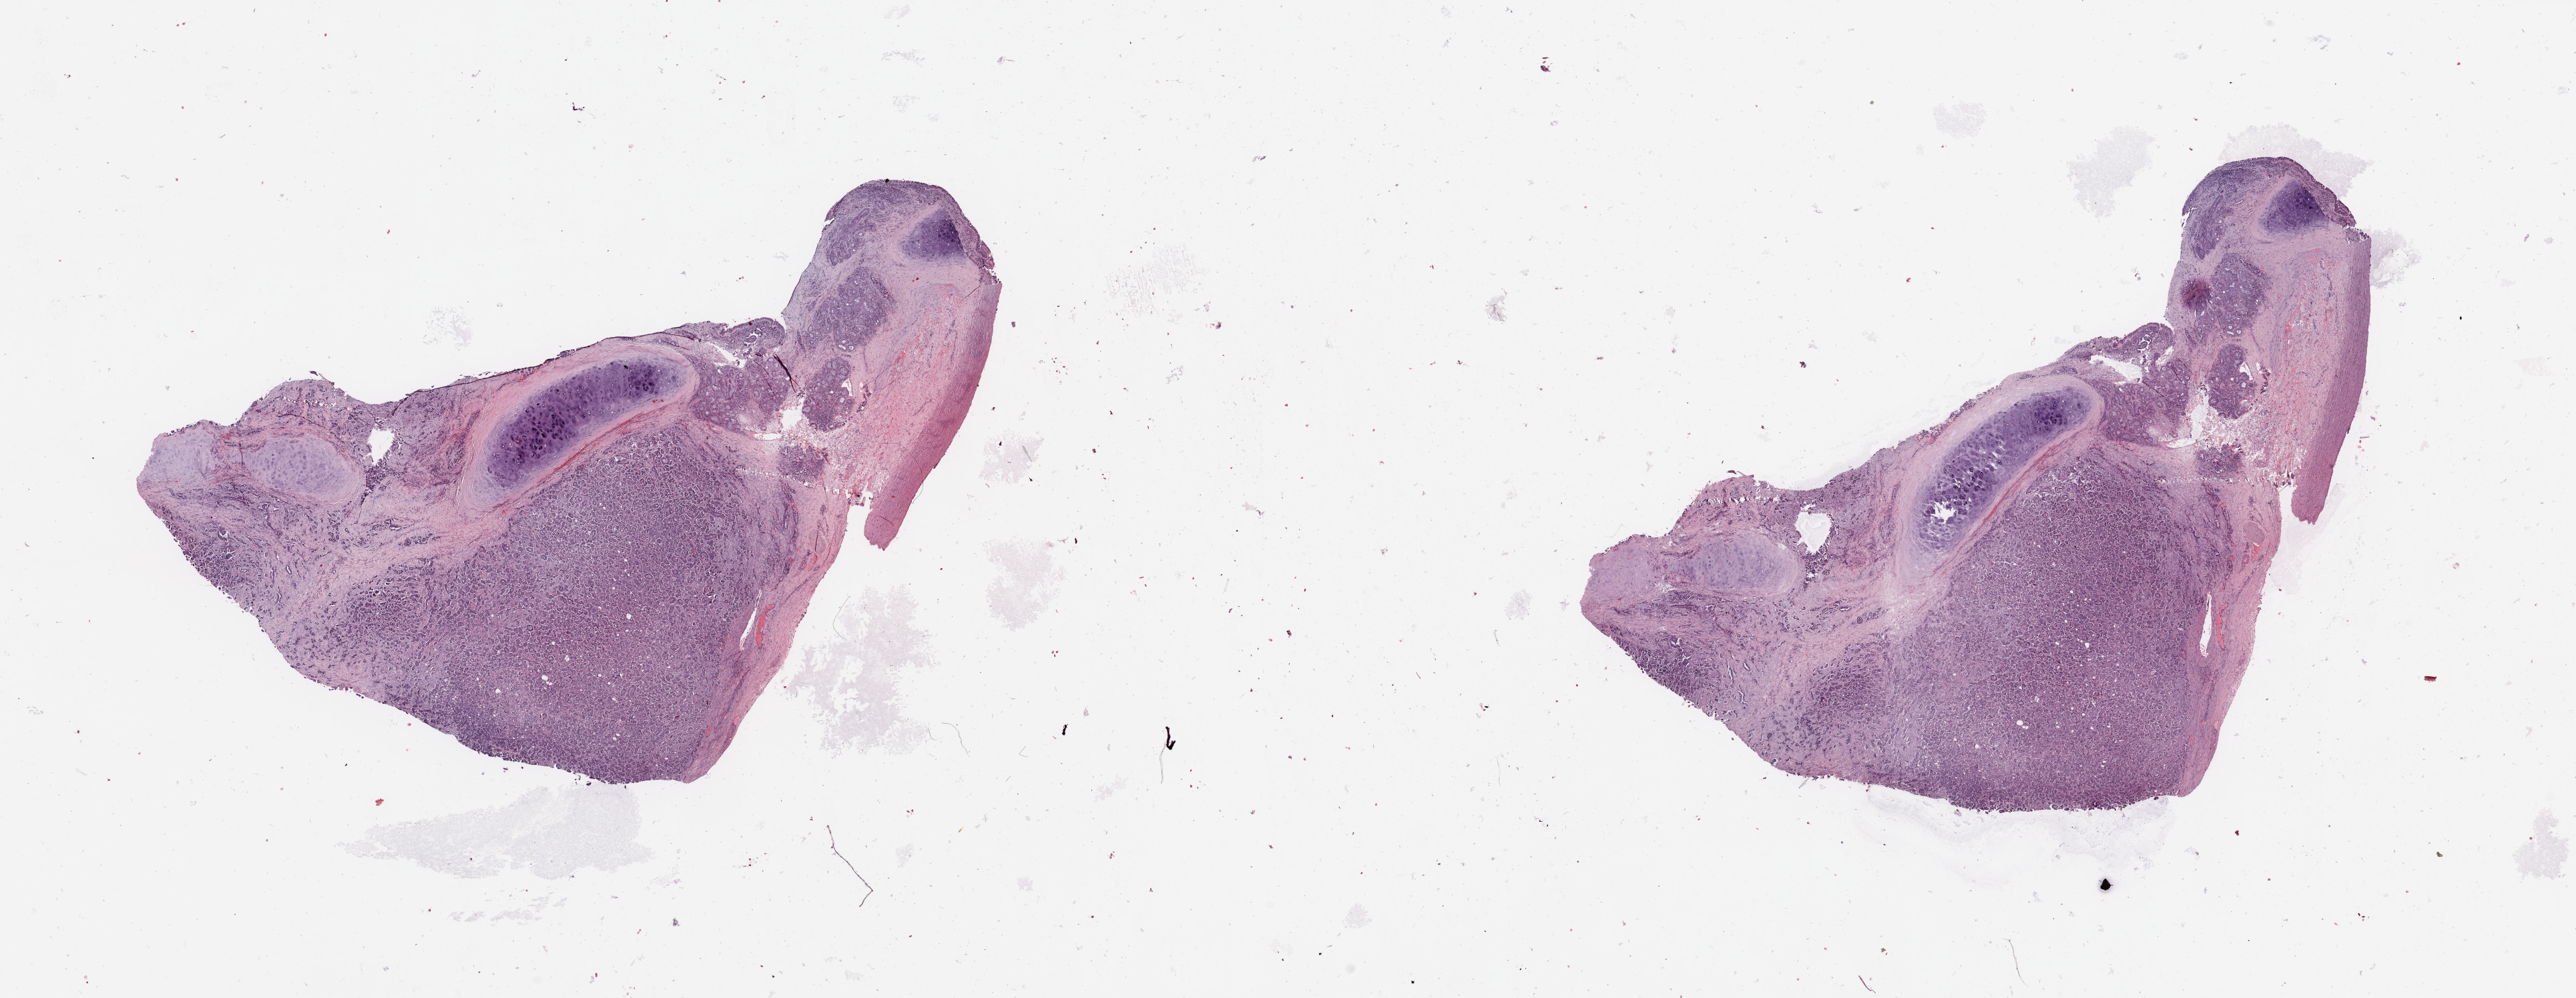
Digitized H&E-stained tissue section (whole slide), low-resolution overview of the scanned area, about 30.5 x 11.8 mm (slide scanned at 20x); lung, tumour tissue. Male, 39 y/o. Histologic grade: G2 (moderately differentiated).
Histologic diagnosis: Adenocarcinoma, NOS. AJCC pathologic stage: IIIA.